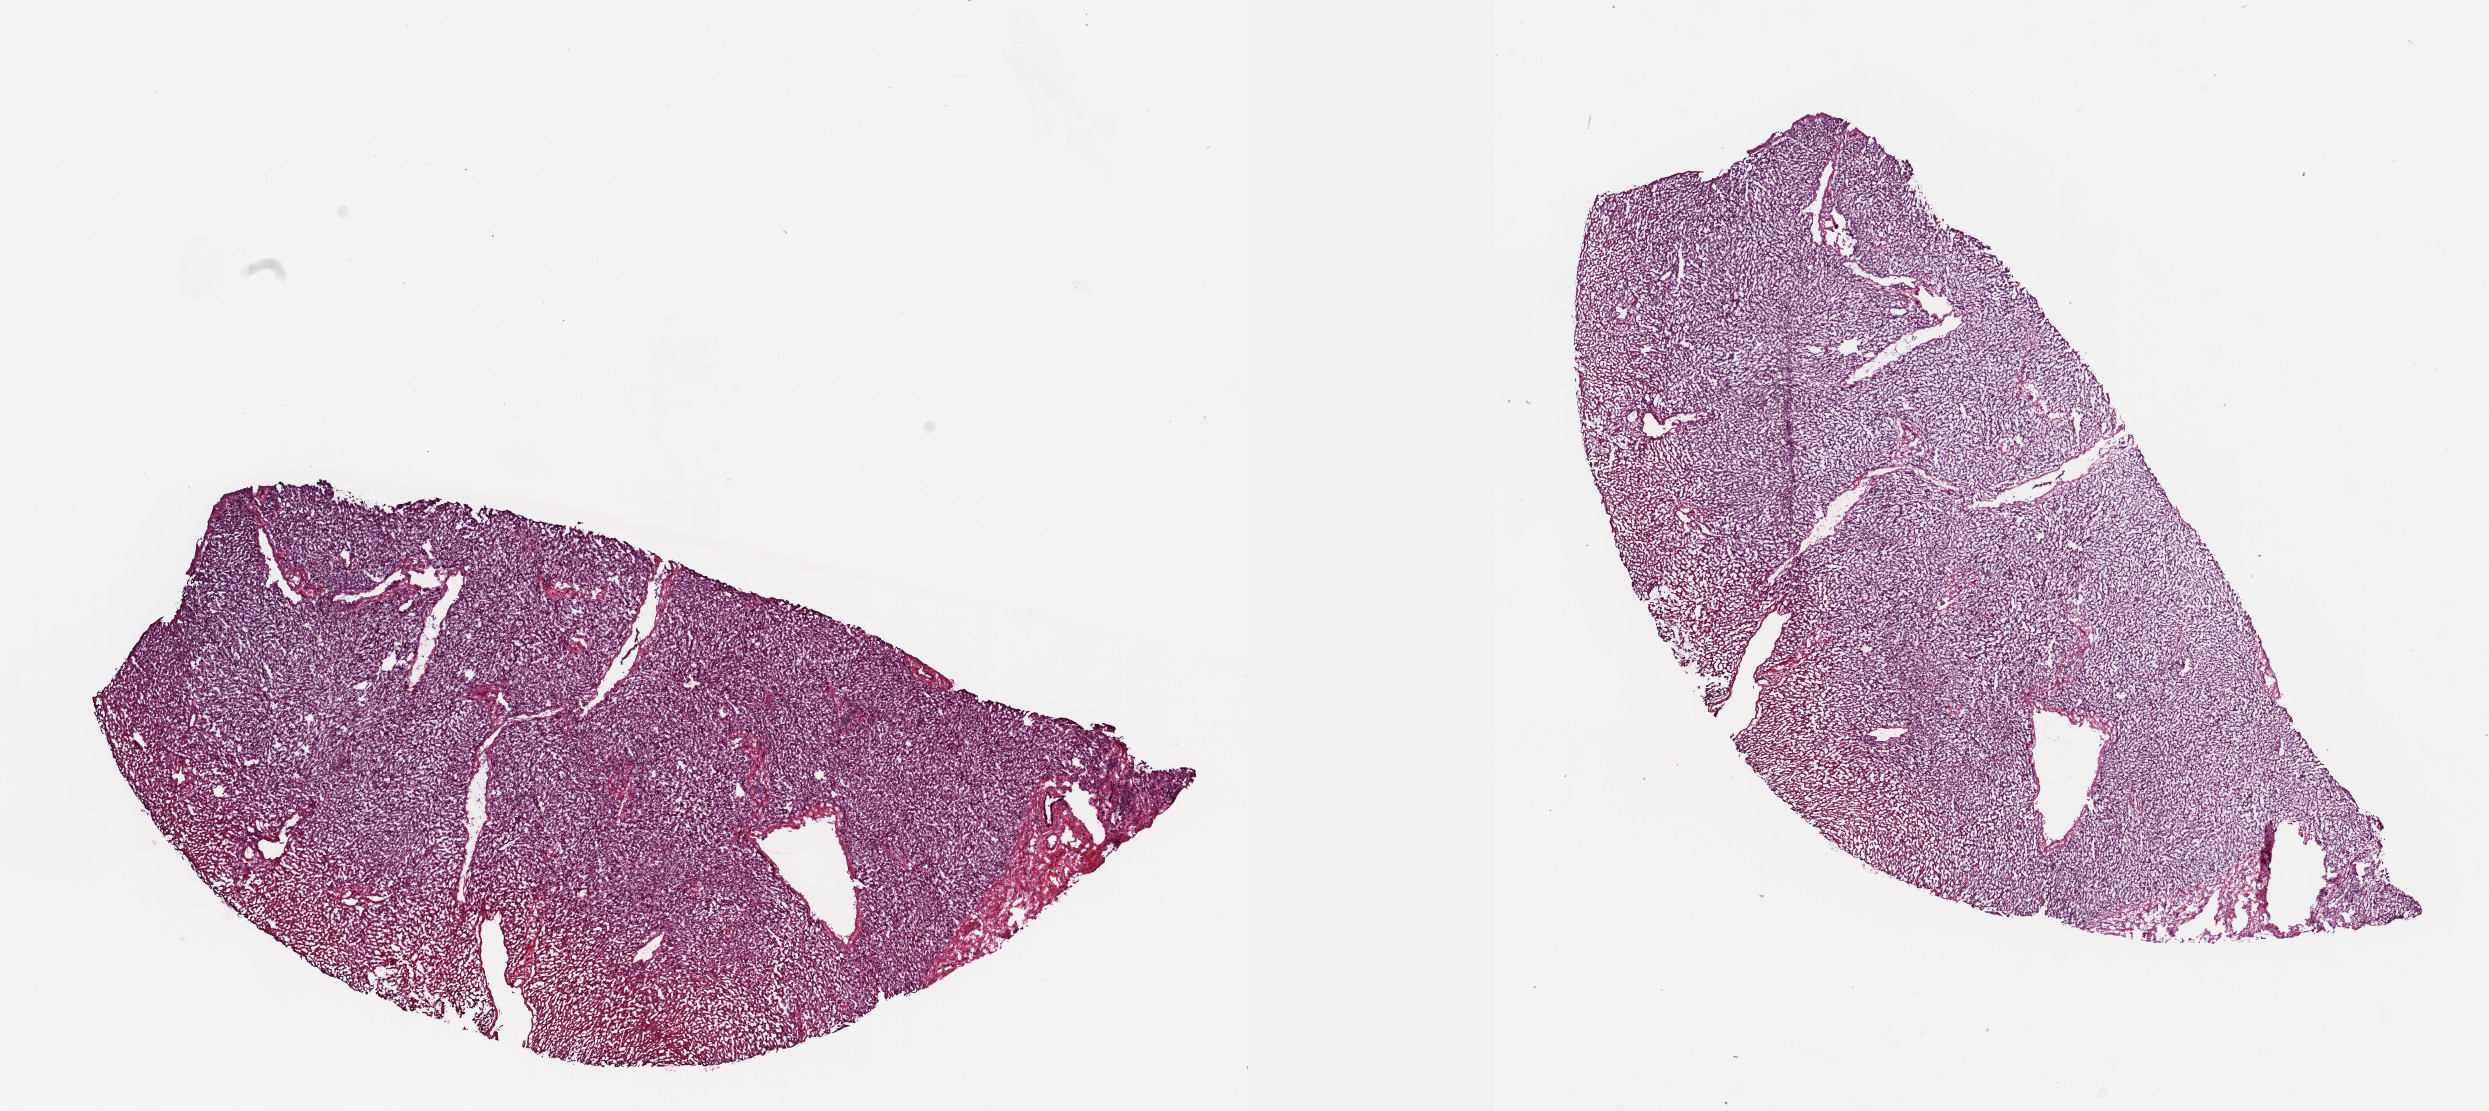
Whole-slide histology image, H&E, a low-resolution overview of the entire scanned area, about 20.1 x 9.0 mm (from a 20x scan); frozen section from the top of the tissue portion; bile duct, solid tissue normal (non-tumour tissue) sample. Male patient; age at initial diagnosis 62 years. Slide review estimates, as recorded: tumour cells 0%, tumour nuclei 0%, normal cells 70%, stromal cells 30%, necrosis 0%. Inflammatory infiltration, as recorded: lymphocyte infiltration 4%, monocyte infiltration 1%, neutrophil infiltration 3%.
• this section: solid tissue normal sample (biorepository sample class)
• patient diagnosis: Cholangiocarcinoma